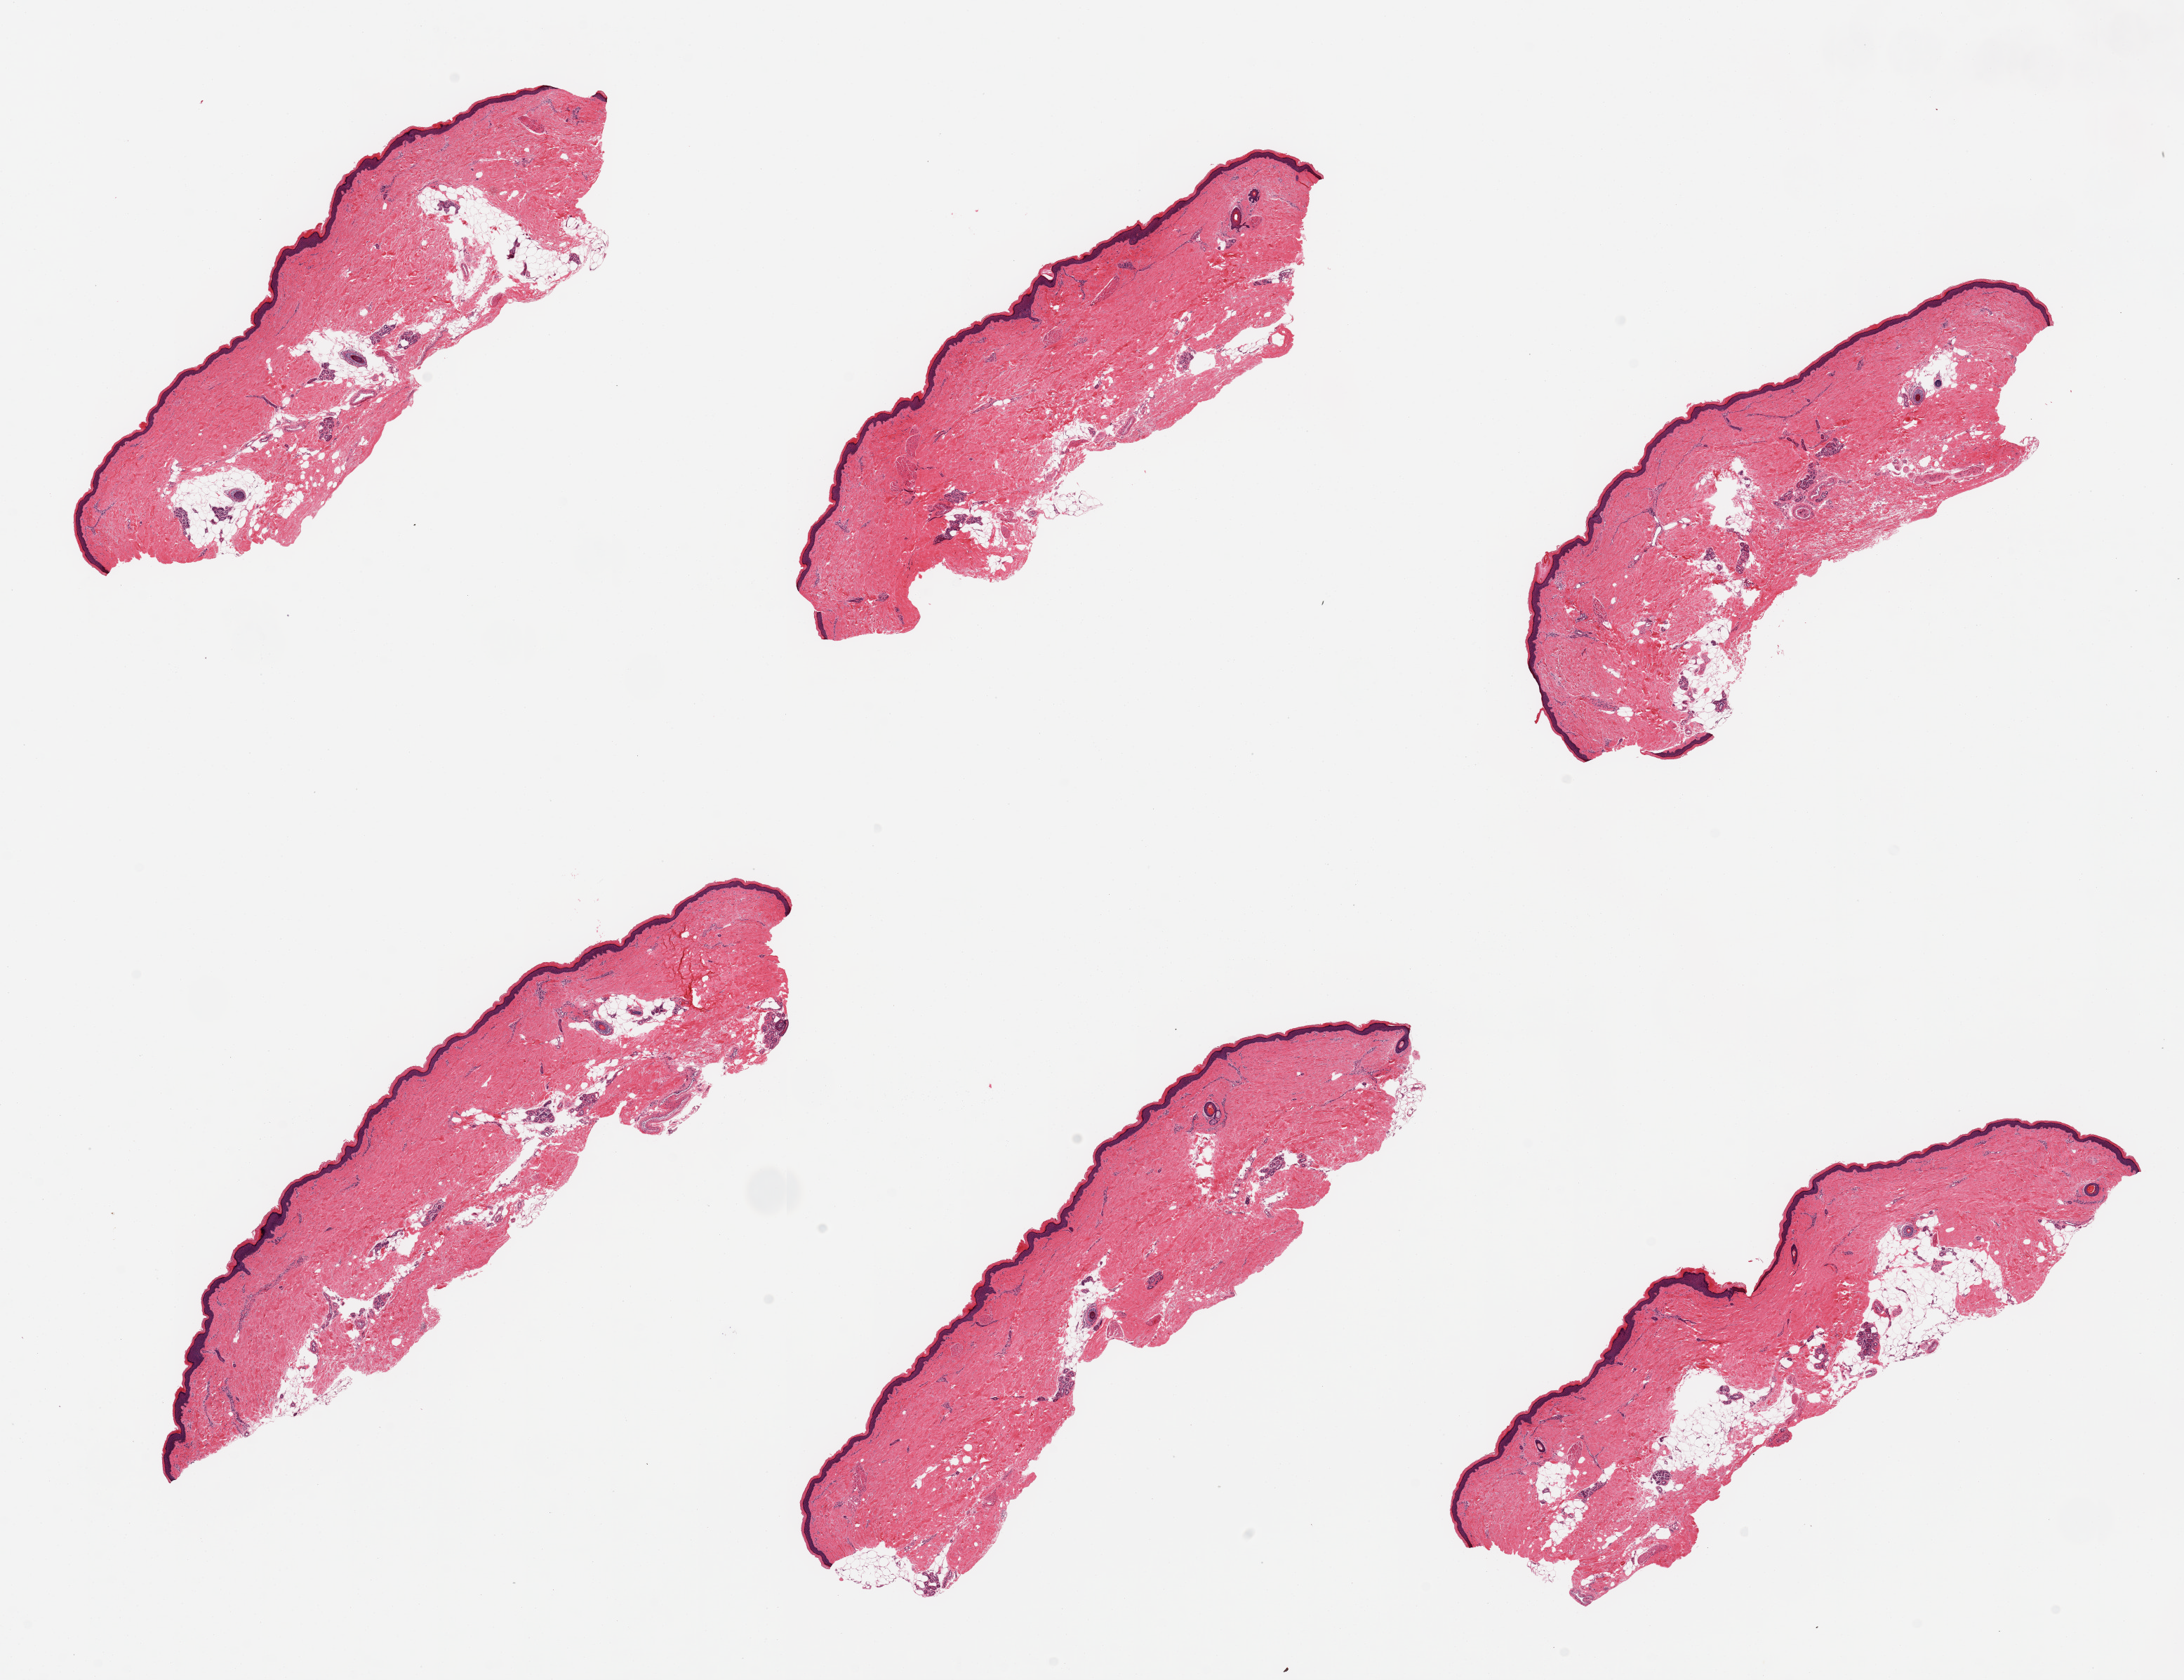
Digitized hematoxylin and eosin (H&E)-stained section — low-resolution overview of the scanned area, about 24.6 x 18.9 mm (slide scanned at 20x); PAXgene-fixed paraffin-embedded (PFPE) section; target tissue: skin of lower leg; donor tissue sample. Donor: female.
Pathologist's review note for this sample: 6 pieces, squamous epithelium is ~60 microns; minimal dermal fat.